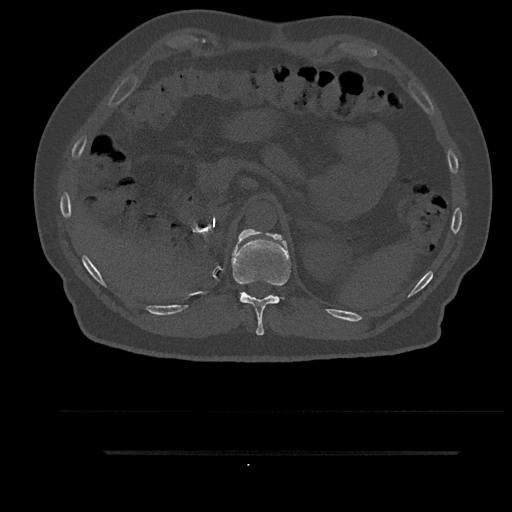
CT including the spine, one axial slice. Reconstruction kernel Br40s/3. Bone window (W 1800 / L 400 HU). 512 × 512 image matrix. Male patient, age 63 years. From the clinical record (not read from this slice): primary cancer: renal.
Outlined on this slice (semi-automatically segmented with operator editing):
- T11 vertebra: bounding box (x1, y1, x2, y2) in pixels: (232, 229, 291, 335)
- T12 vertebra: (238, 230, 256, 241)